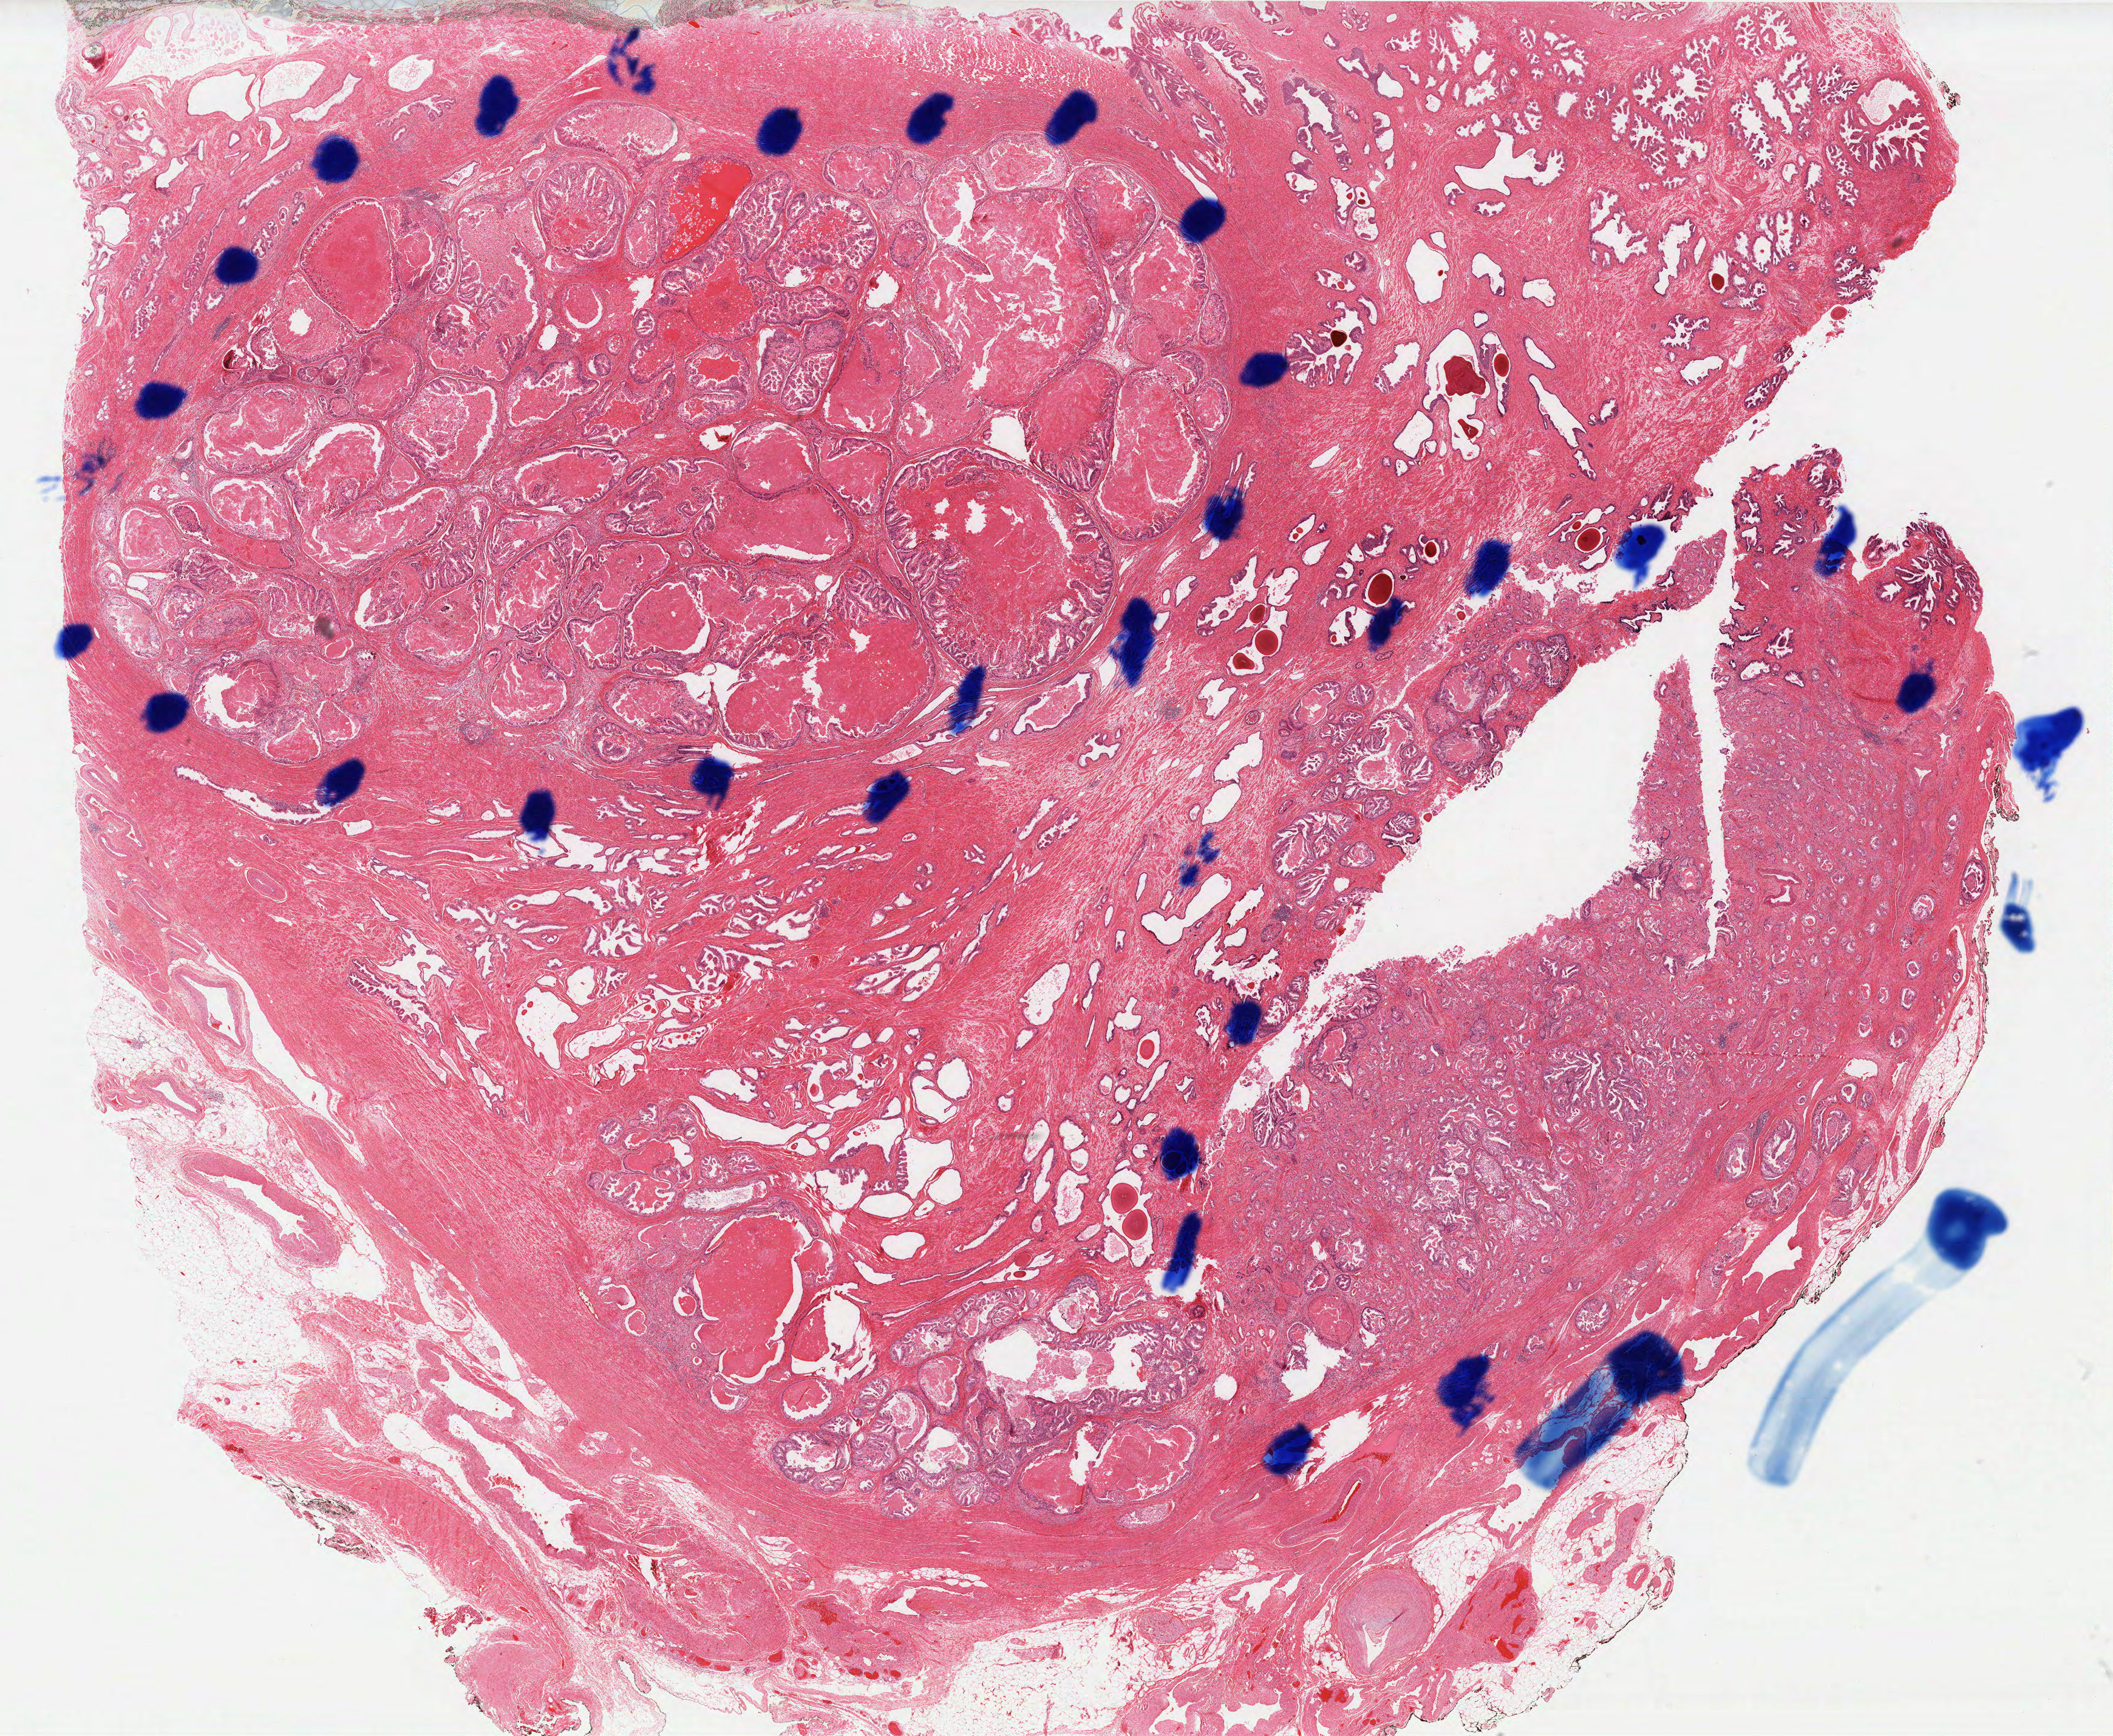
Whole-slide histology image, H&E — shown as a low-resolution overview of the whole scanned area (about 27.9 x 22.9 mm, acquisition: 40x scan); FFPE section; sample: primary tumour, prostate. Male, age 60 years at initial diagnosis. Gleason score: 8 (5+3).
Laterality: bilateral. Diagnosis: Infiltrating duct carcinoma, NOS (prostate gland). Lymph nodes positive (case pathology): 0 of 12 examined.